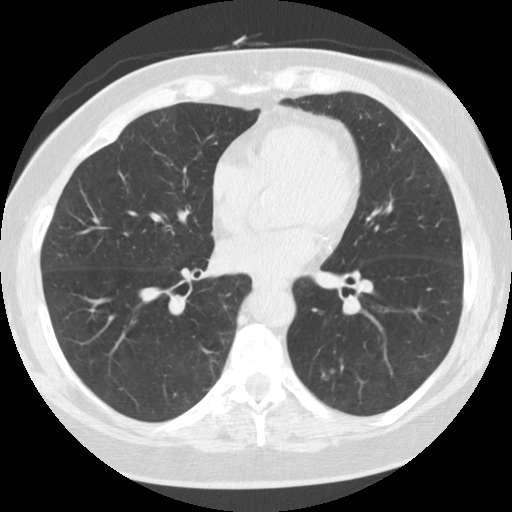
Axial slice from a low-dose chest CT screening exam. Baseline annual screen. Lung window (W 1500 / L -600 HU). 2.5 mm slice thickness. Slice 68 of 115 in the series. Female, age 59 years at enrolment.
Lesion marked by an expert reader, box from (x=289, y=349) to (x=358, y=415) px. The screening reader recorded 5 non-calcified nodules or masses ≥4 mm on this exam; which of them this box marks is not recorded. Official screen result: positive, change unspecified: nodule(s) >= 4 mm or enlarging nodule(s), mass(es), or other non-specific abnormalities suspicious for lung cancer. Participant outcome: lung cancer diagnosed 707 days after this screen (after the third annual screen) — adenocarcinoma, NOS, left lower lobe, poorly differentiated (G3), stage IA (AJCC 6th edition), 15 mm at pathology.